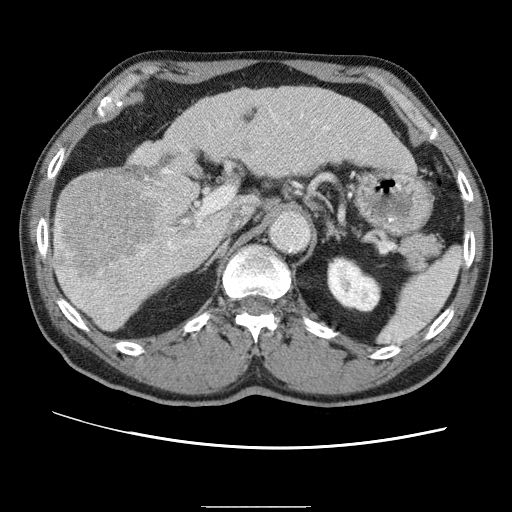
Contrast-enhanced abdominal CT (liver protocol), one axial slice; position 30 of 75 along the scan axis; reconstruction kernel STANDARD; 120 kVp; one of 2 acquisitions stored at this slice position; soft-tissue window (W 400 / L 40 HU); 2.5 mm slice thickness; 512 × 512 image matrix. From the clinical record (not read from this slice): diagnosis: hepatocellular carcinoma (patient treated with transarterial chemoembolisation; whether this scan precedes or follows treatment is not stated here); TNM stage (as recorded): Stage-II; Child-Pugh class: A; tumour differentiation: well differentiated; tumour nodularity: multinodular.
Structures marked on this image (semi-automatically segmented with operator editing):
- liver parenchyma outside the tumour (the mass and vessels are separate outlines, so this box may not span the whole liver): box from (x=54, y=88) to (x=408, y=330) px
- mass: (x=55, y=168)–(x=157, y=282)
- liver vessels: (x=61, y=121)–(x=323, y=280)